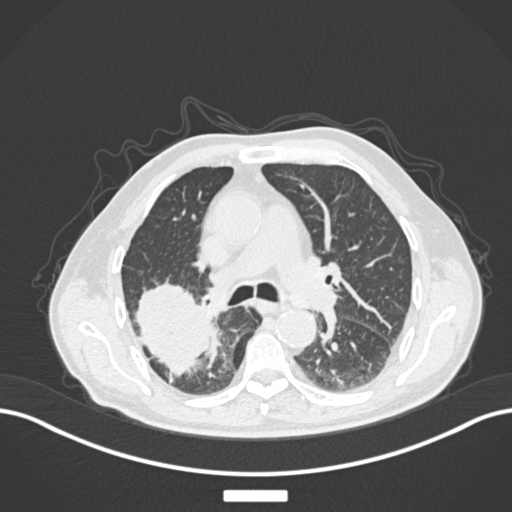
Chest CT, one axial slice; slice 107 of 201 in the series (ordered by position); reconstruction kernel B30f; lung window (W 1500 / L -600 HU); 512 × 512 image matrix, field of view 400 × 400 mm. Patient: male, 72 years. From the clinical record (not read from this slice): clinical TNM (as recorded): T3 N2 M0.
Structures marked on this image (bounding box drawn by a radiologist):
- lung tumour (recorded histology: adenocarcinoma): box from (x=129, y=276) to (x=220, y=383) px